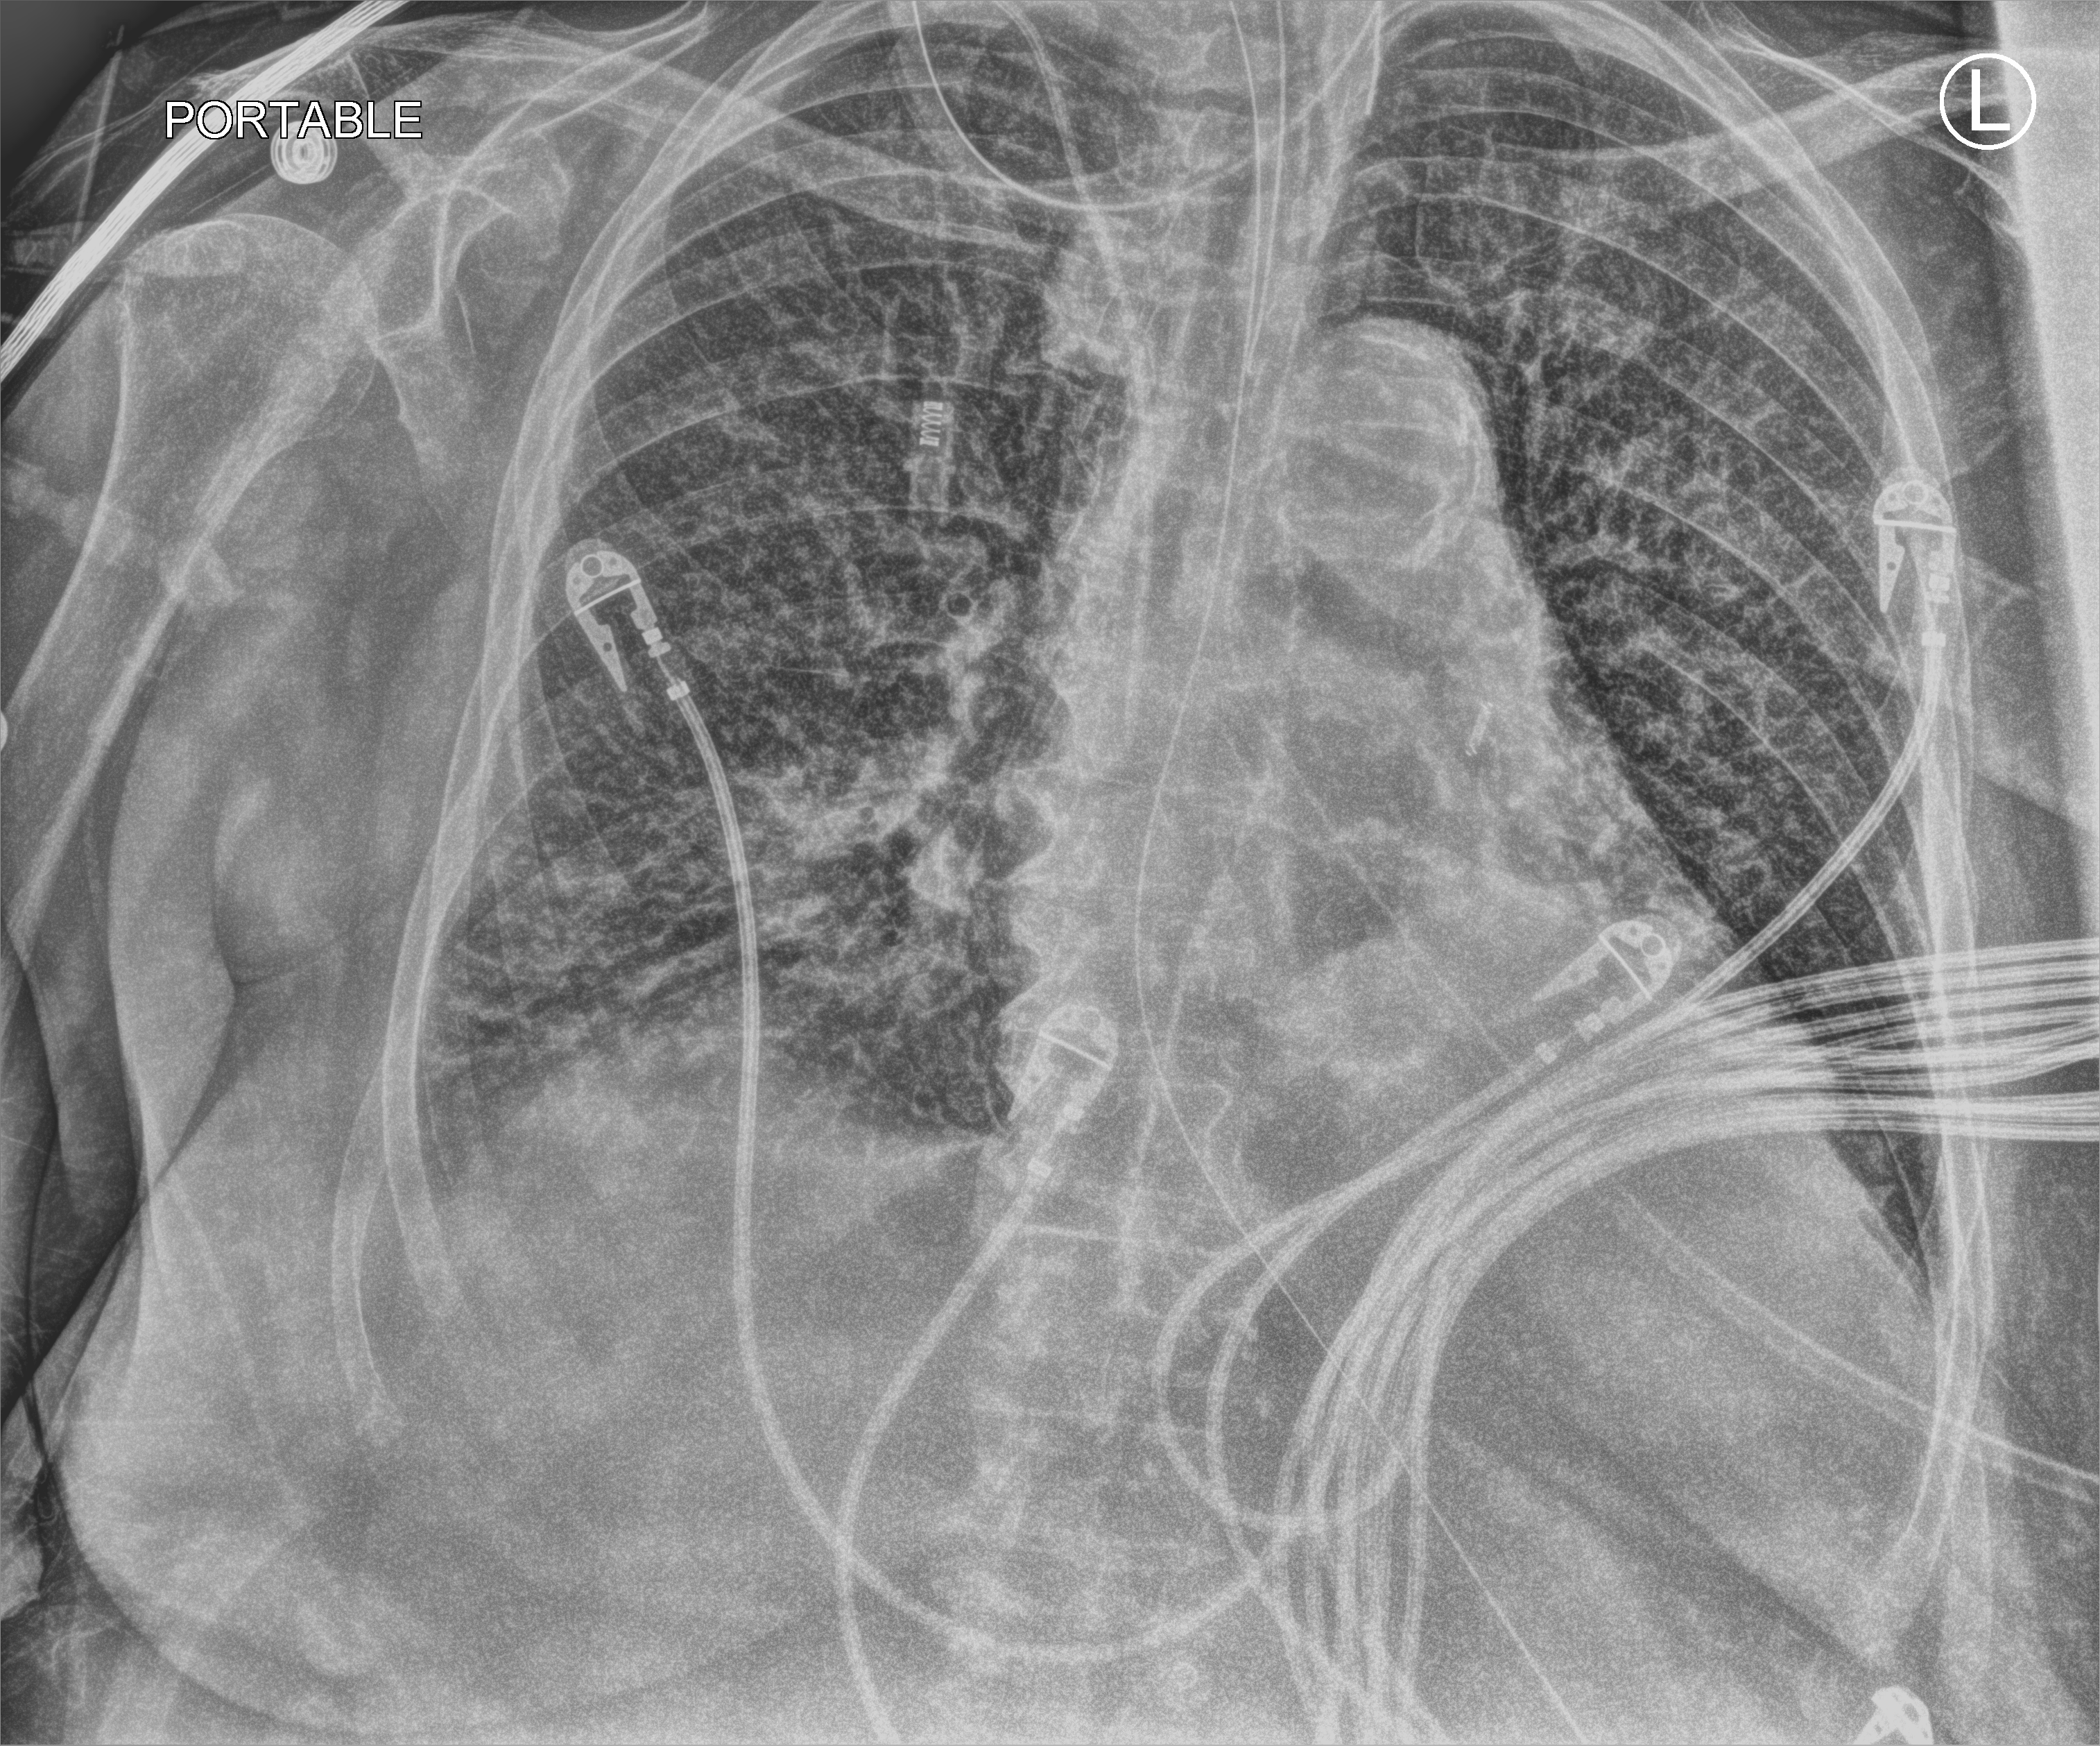
Bedside chest radiograph (computed radiography), anteroposterior (AP) projection. Patient hospitalised with COVID-19; female, aged 75–90 years.
Admission-level facts for this patient (not findings on this image; timing relative to this image not recorded):
- other chronic lung disease (admission record): no
- admitted to intensive care during this hospital stay: yes
- mechanically ventilated during this hospital stay: yes